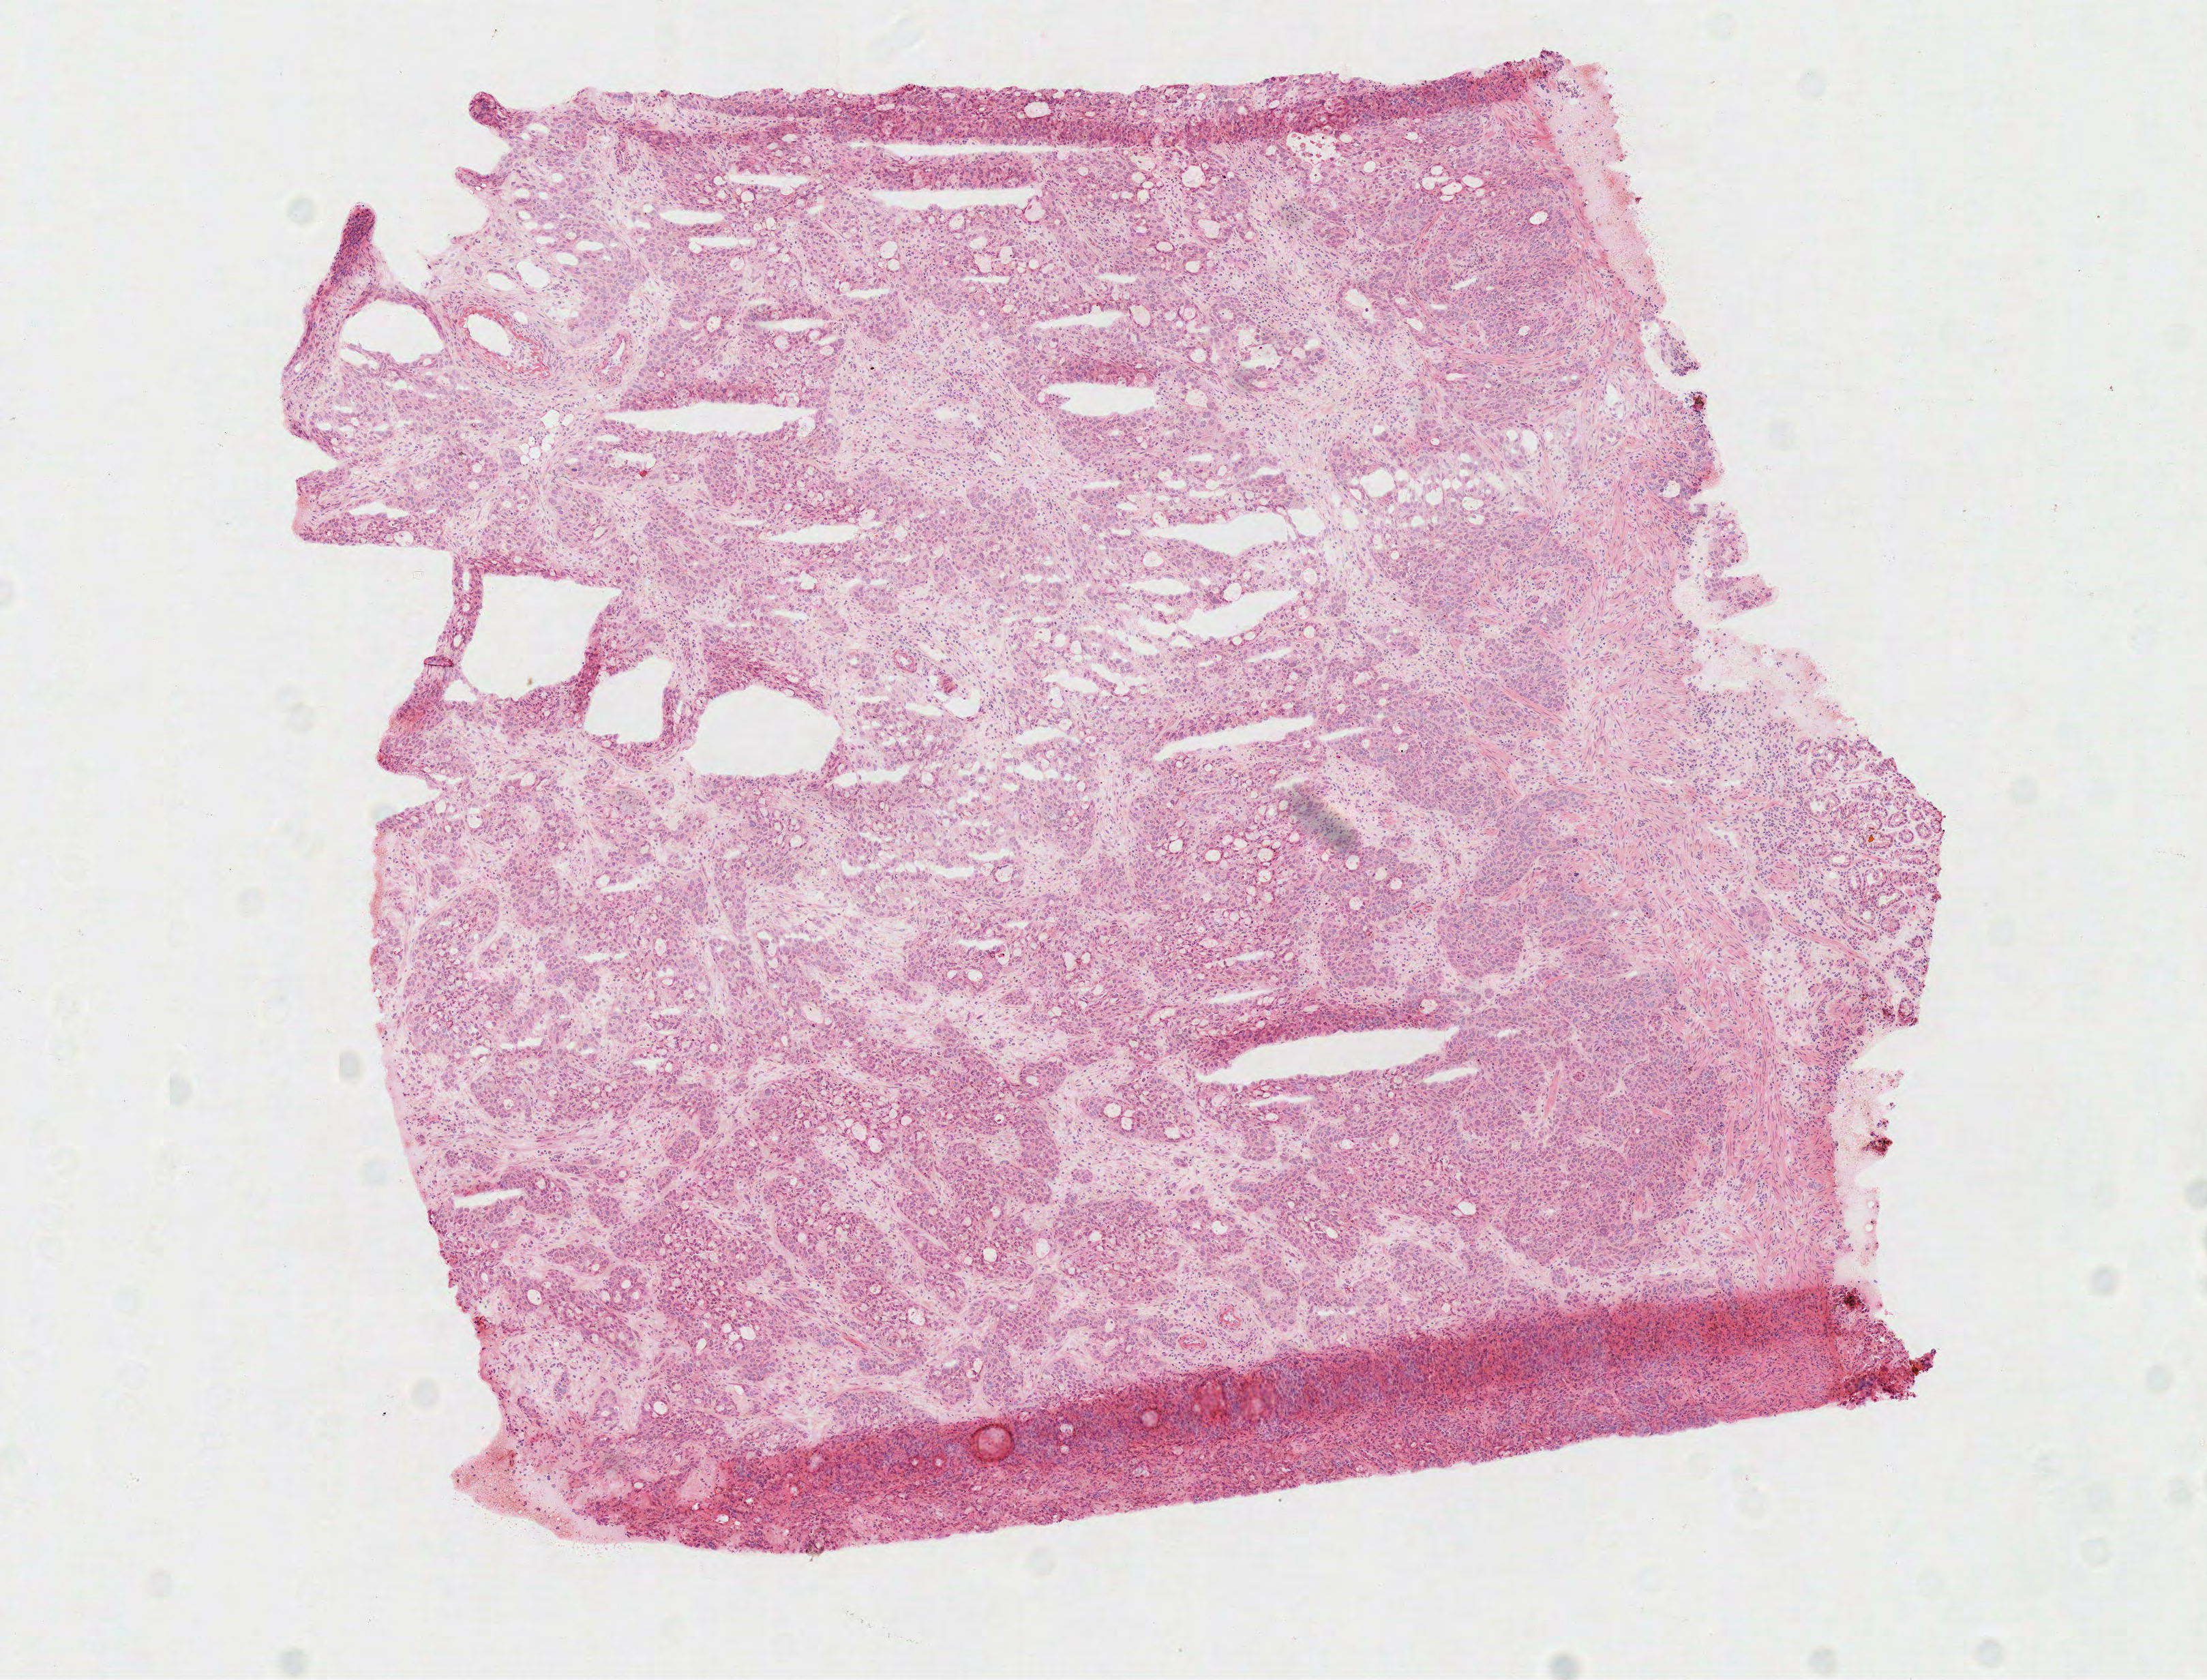
Digitized Hematoxylin and eosin (H&E) stained tissue section (whole slide), low-resolution overview of the scanned area, about 6.4 x 4.8 mm, frozen section from the top of the tissue portion, stomach, primary tumour sample. Patient: female, age at initial diagnosis 64 years. Composition of this section per pathologist review: tumour cells 82%, tumour nuclei 80%.
Diagnosis: Carcinoma, diffuse type (cardia, NOS).